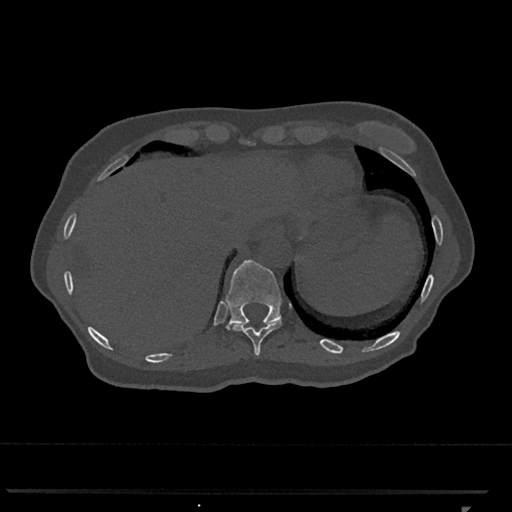
CT including the spine, one axial slice. Slice 543 of 793 in the series (ordered by position). Reconstruction kernel Br40s/3. 120 kVp. Bone window (W 1800 / L 400 HU). 512 × 512 image matrix, field of view 380 × 380 mm. Patient: female, 62 years. From the clinical record (not read from this slice): primary cancer: renal.
Annotated regions visible in this slice (semi-automatic segmentation, software-assisted and operator-edited):
- T10 vertebra: bounding box <229,322,282,357> (left, top, right, bottom; pixels)
- T11 vertebra: <225,260,282,330>